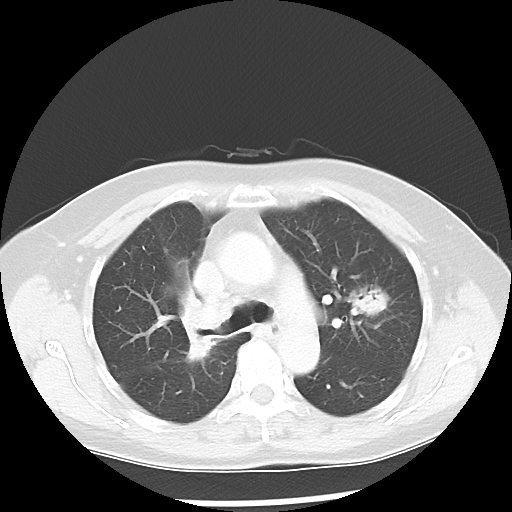
Chest CT, one axial slice. Slice 34 of 52 in the series (ordered by position). 100 kVp. Lung window (W 1500 / L -600 HU). 5 mm slice thickness. 512 × 512 image matrix, field of view 328 × 328 mm. Patient: female, 60 years. From the clinical record (not read from this slice): clinical TNM (as recorded): T2 N1 M1a.
Annotated regions visible in this slice (bounding box drawn by a radiologist):
- lung tumour (recorded histology: adenocarcinoma): box from (x=172, y=274) to (x=218, y=372) px